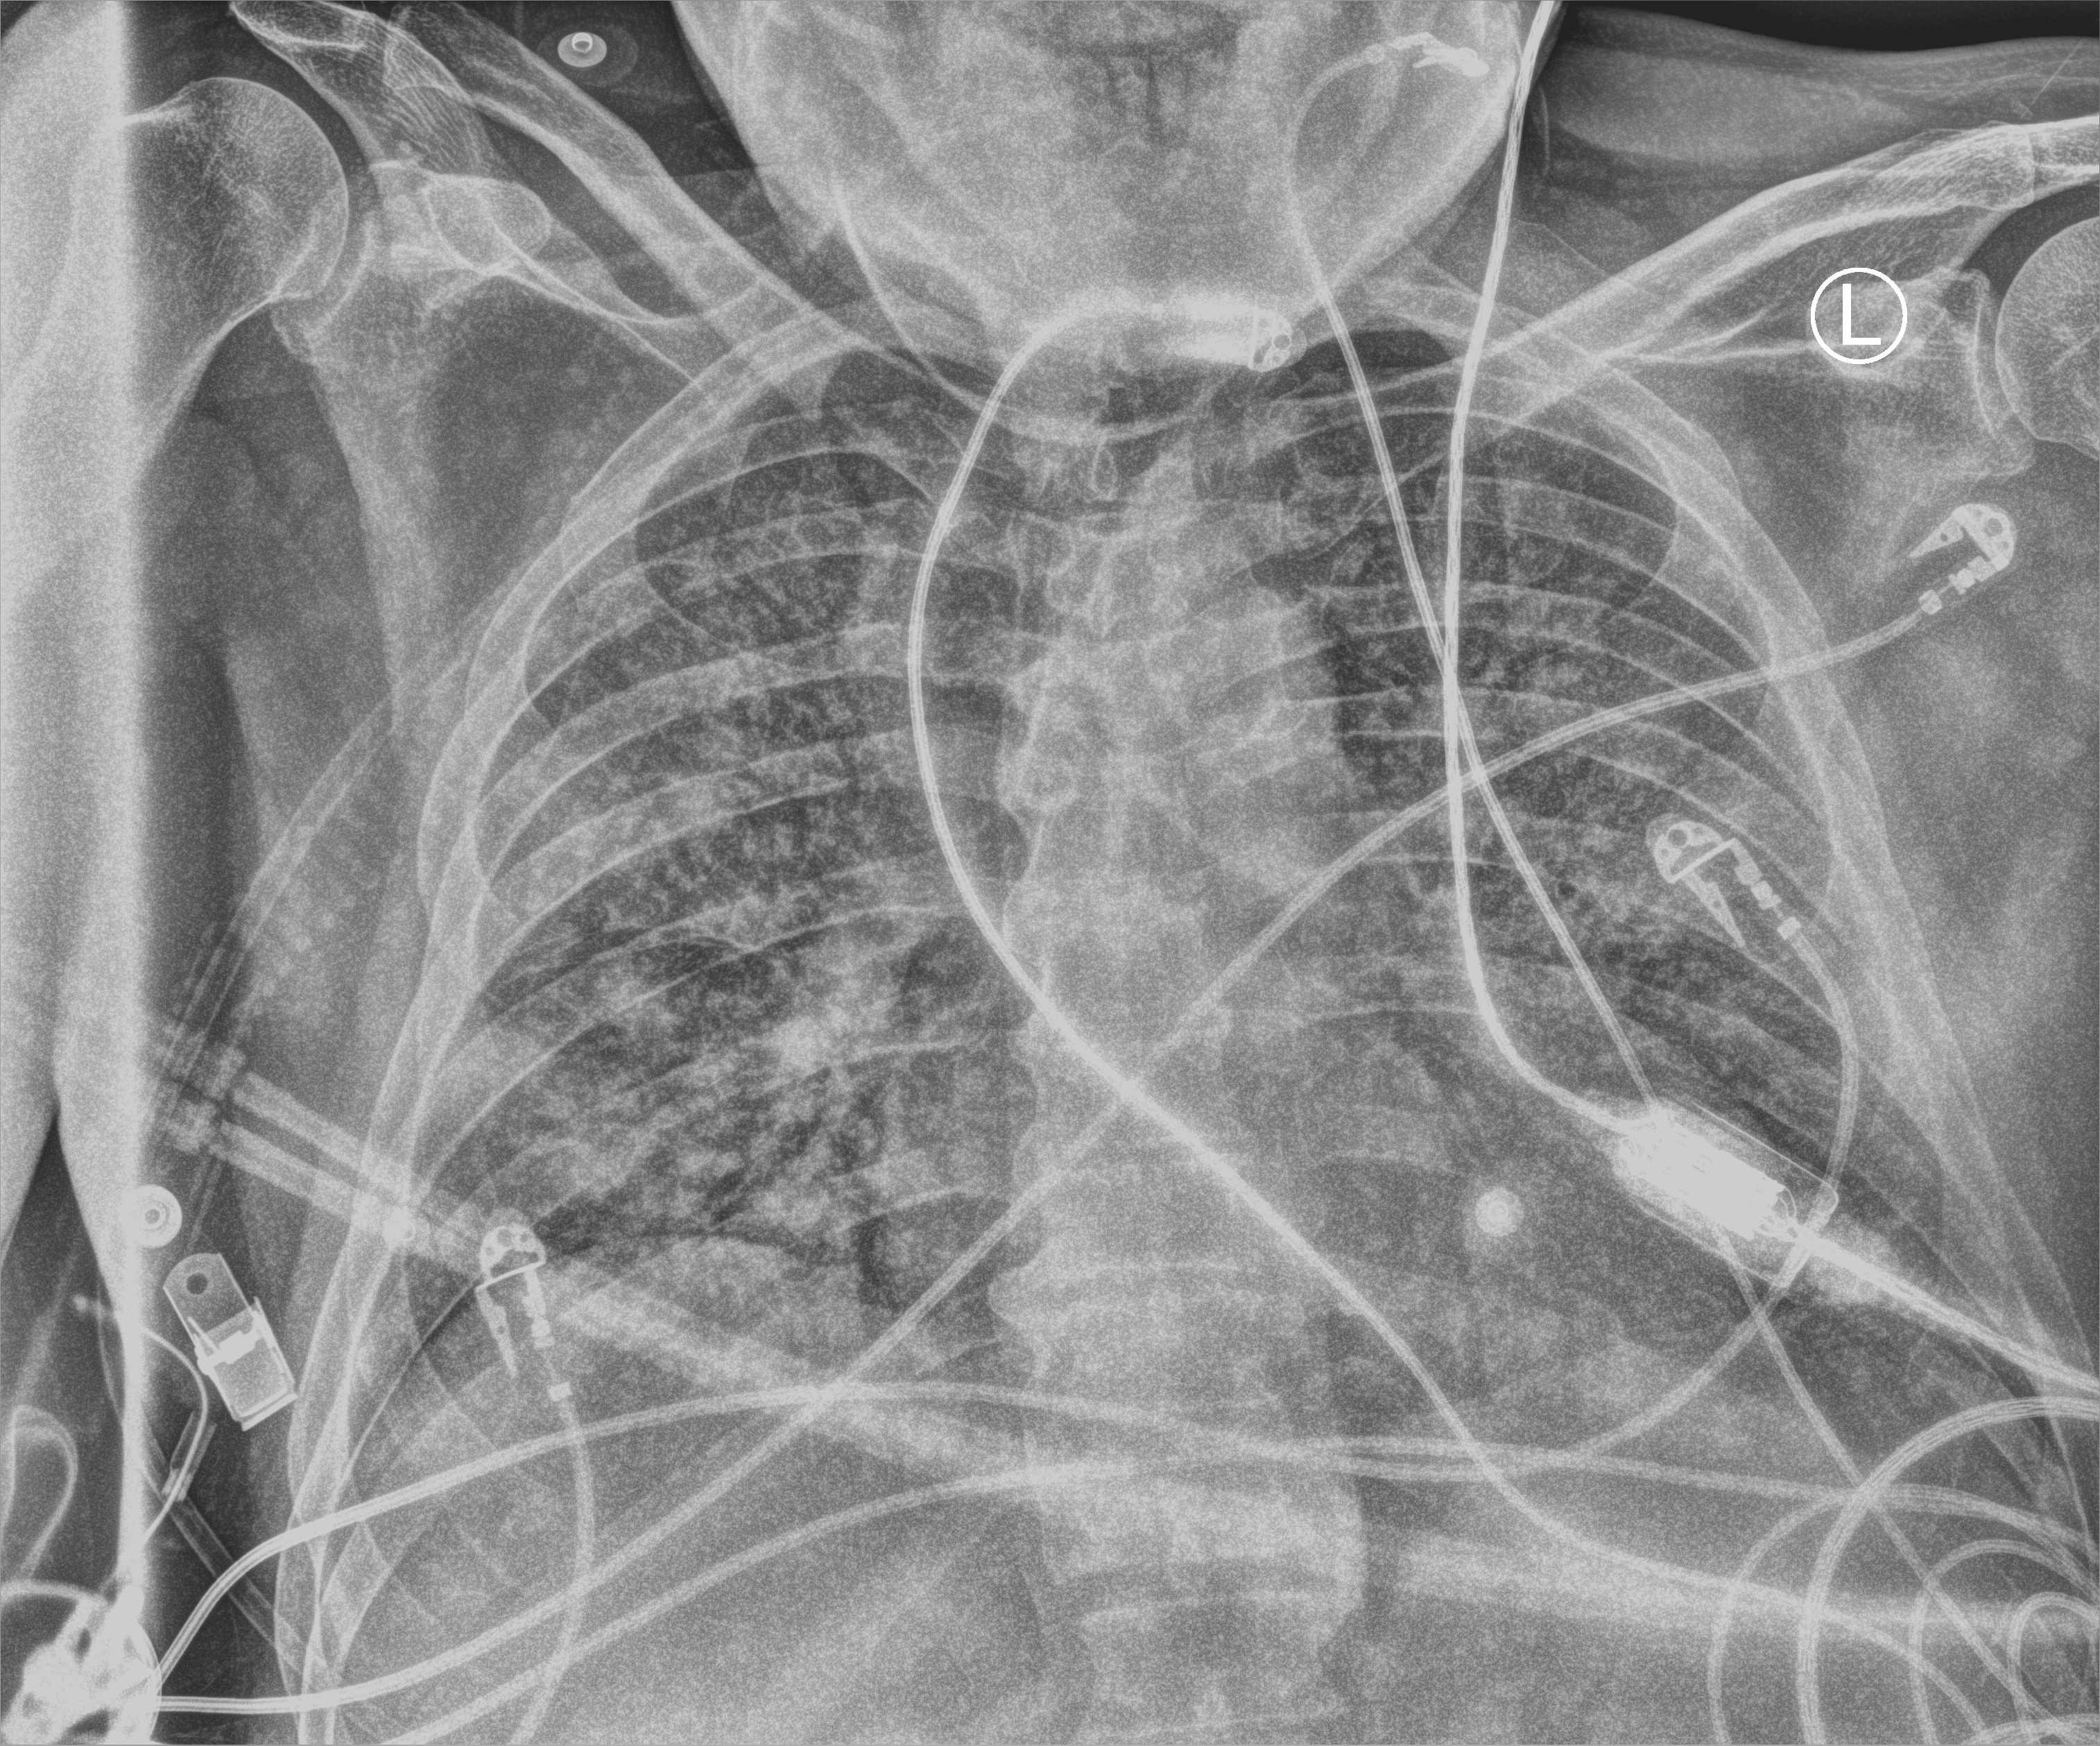
Portable chest radiograph. Patient hospitalised with COVID-19; male, aged 60–74 years.
Admission-level facts for this patient (not findings on this image; timing relative to this image not recorded): chronic kidney disease (admission record): no; mechanically ventilated during this hospital stay: yes.